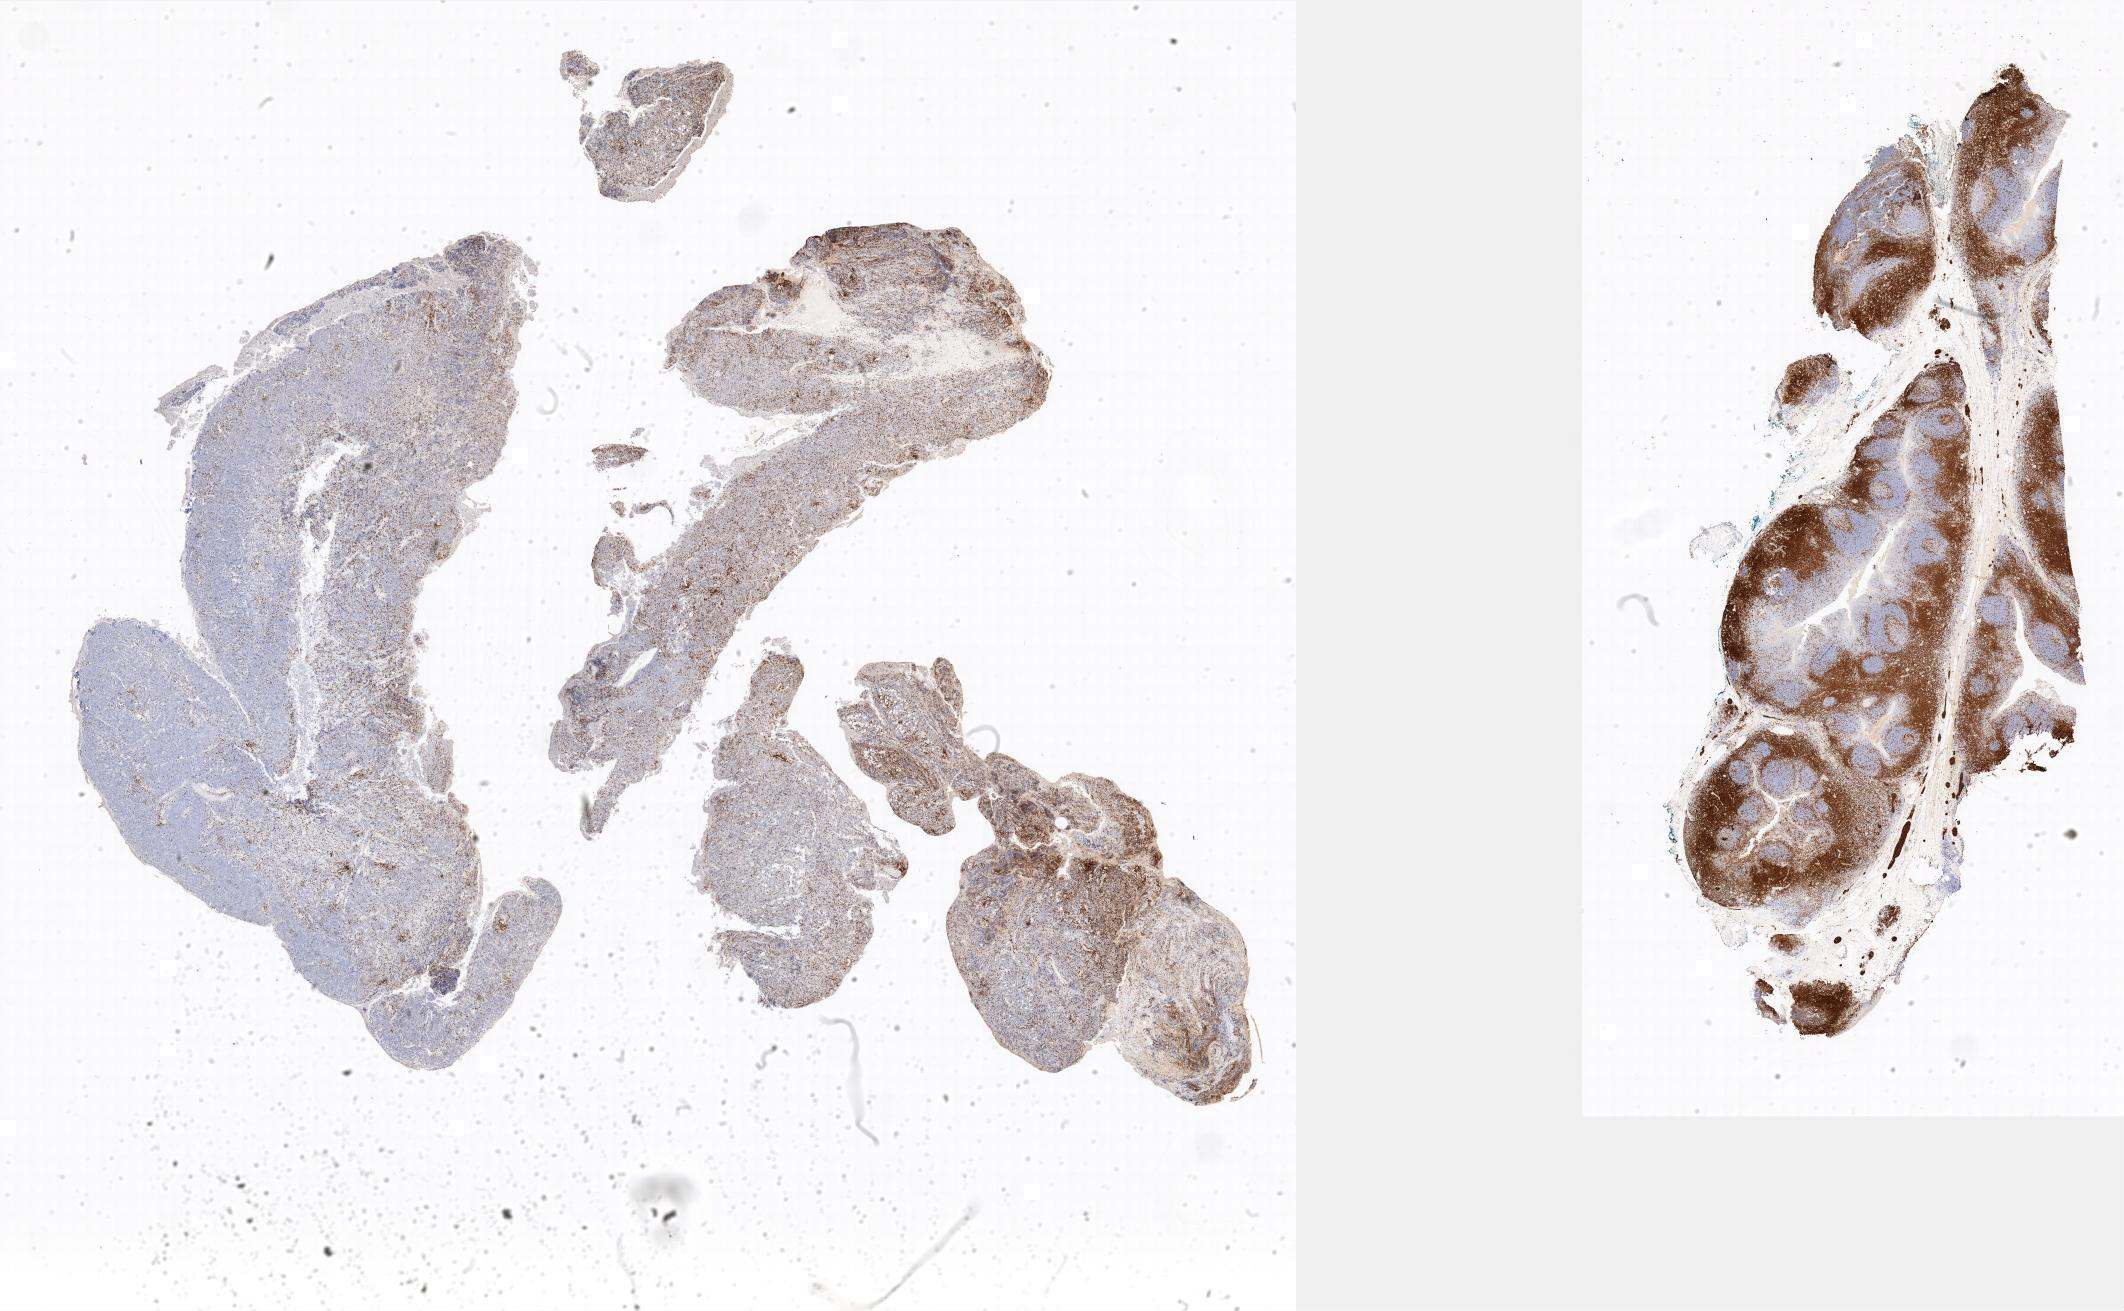
Immunohistochemistry (IHC) whole-slide image stained for CD3 — a low-resolution overview of the entire scanned area; tumor tissue; site: abdomen proper. Male patient; age at initial diagnosis 5 years.
• diagnosis: Burkitt lymphoma, NOS